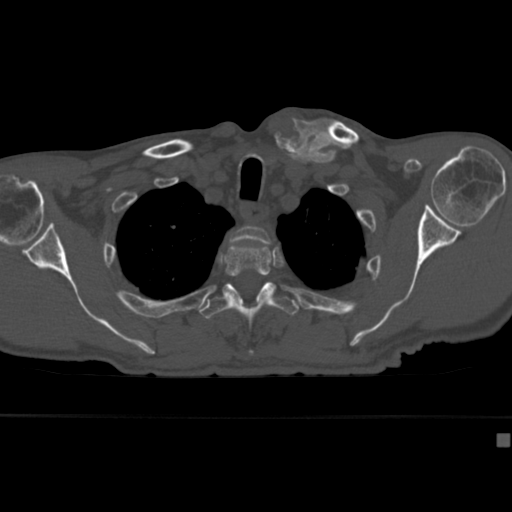
CT including the spine, one axial slice. Position 329 of 430 along the scan axis. Reconstruction kernel Br40s. 120 kVp. Bone window (W 1800 / L 400 HU). 1.5 mm slice thickness. 512 × 512 image matrix, field of view 337 × 337 mm. Male patient, age 64 years. Case-level facts recorded for this patient, not image findings: primary cancer: uterus; vertebrae with lytic lesions (as recorded): T1, T4, T5, T7, L5.
Annotated regions visible in this slice (semi-automatic segmentation, software-assisted and operator-edited):
- T2 vertebra: bounding box <230,225,271,245> (left, top, right, bottom; pixels)
- T3 vertebra: <224,244,281,285>
- T4 vertebra: <200,282,299,356>